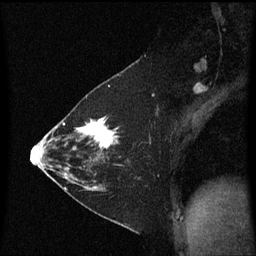
Breast MRI (dynamic contrast-enhanced), one sagittal slice. Slice 35 of 60 in the series (ordered by position). Dynamic contrast-enhanced series, image 2 of 3 at this slice position (ordered by acquisition). 1.5 T. TE 4.2 ms, TR 8.4 ms. 256 × 256 image matrix. Female patient, age 36 years. From the clinical record (not read from this slice): setting: breast cancer imaged before/during neoadjuvant chemotherapy; receptor status: HR-positive, HER2-negative.
Structures marked on this image (semi-automatic segmentation, software-assisted and operator-edited):
- analysis volume of interest (the breast-tissue region the enhancement analysis was run in; not a lesion): box from (x=72, y=116) to (x=119, y=187) px
- tumour enhancement mask (voxels above the 70 % enhancement threshold inside the analysis volume of interest): (x=74, y=118)–(x=119, y=151)